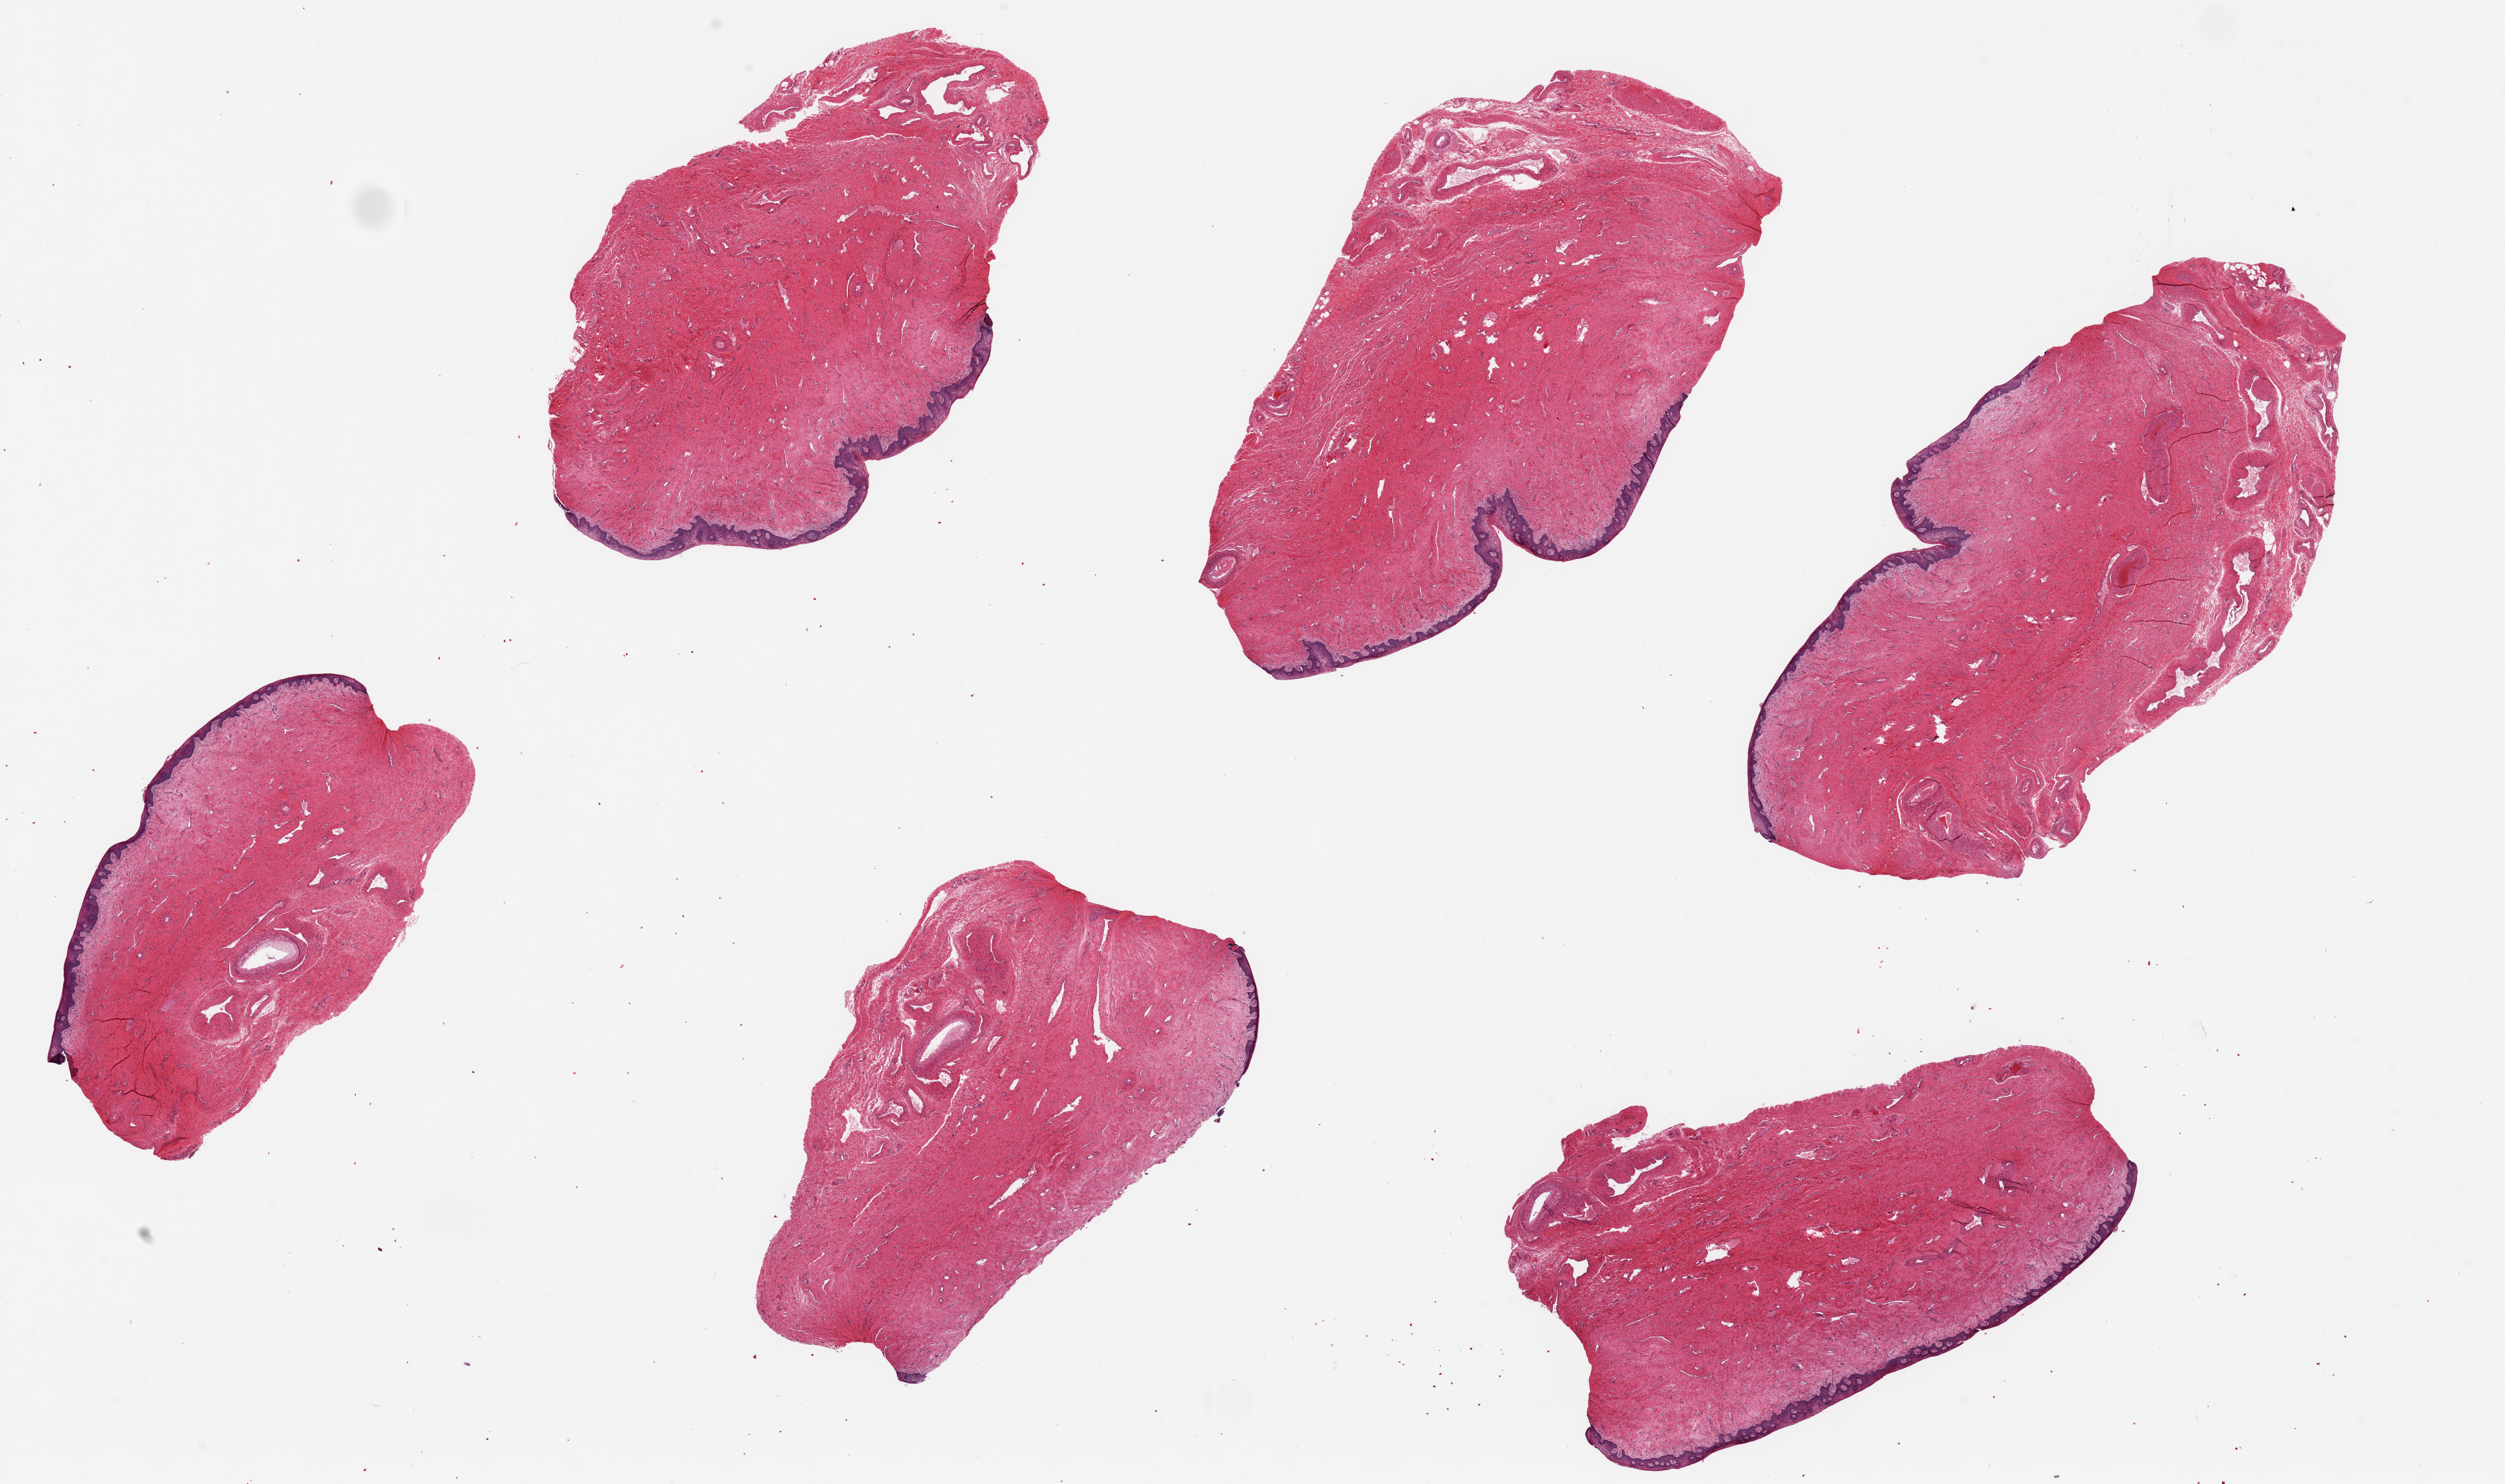
Hematoxylin and eosin (H&E) whole-slide image, whole scanned area (about 30.5 x 18.1 mm) shown as a low-resolution overview. PAXgene-fixed, paraffin-embedded tissue. Sampled site (target tissue): vagina. Donor tissue sample. Female donor.
• pathologist's review note for this sample: 6 pieces, up to 9x5mm; squamous mucosa is ~5% thickness, discontinuous